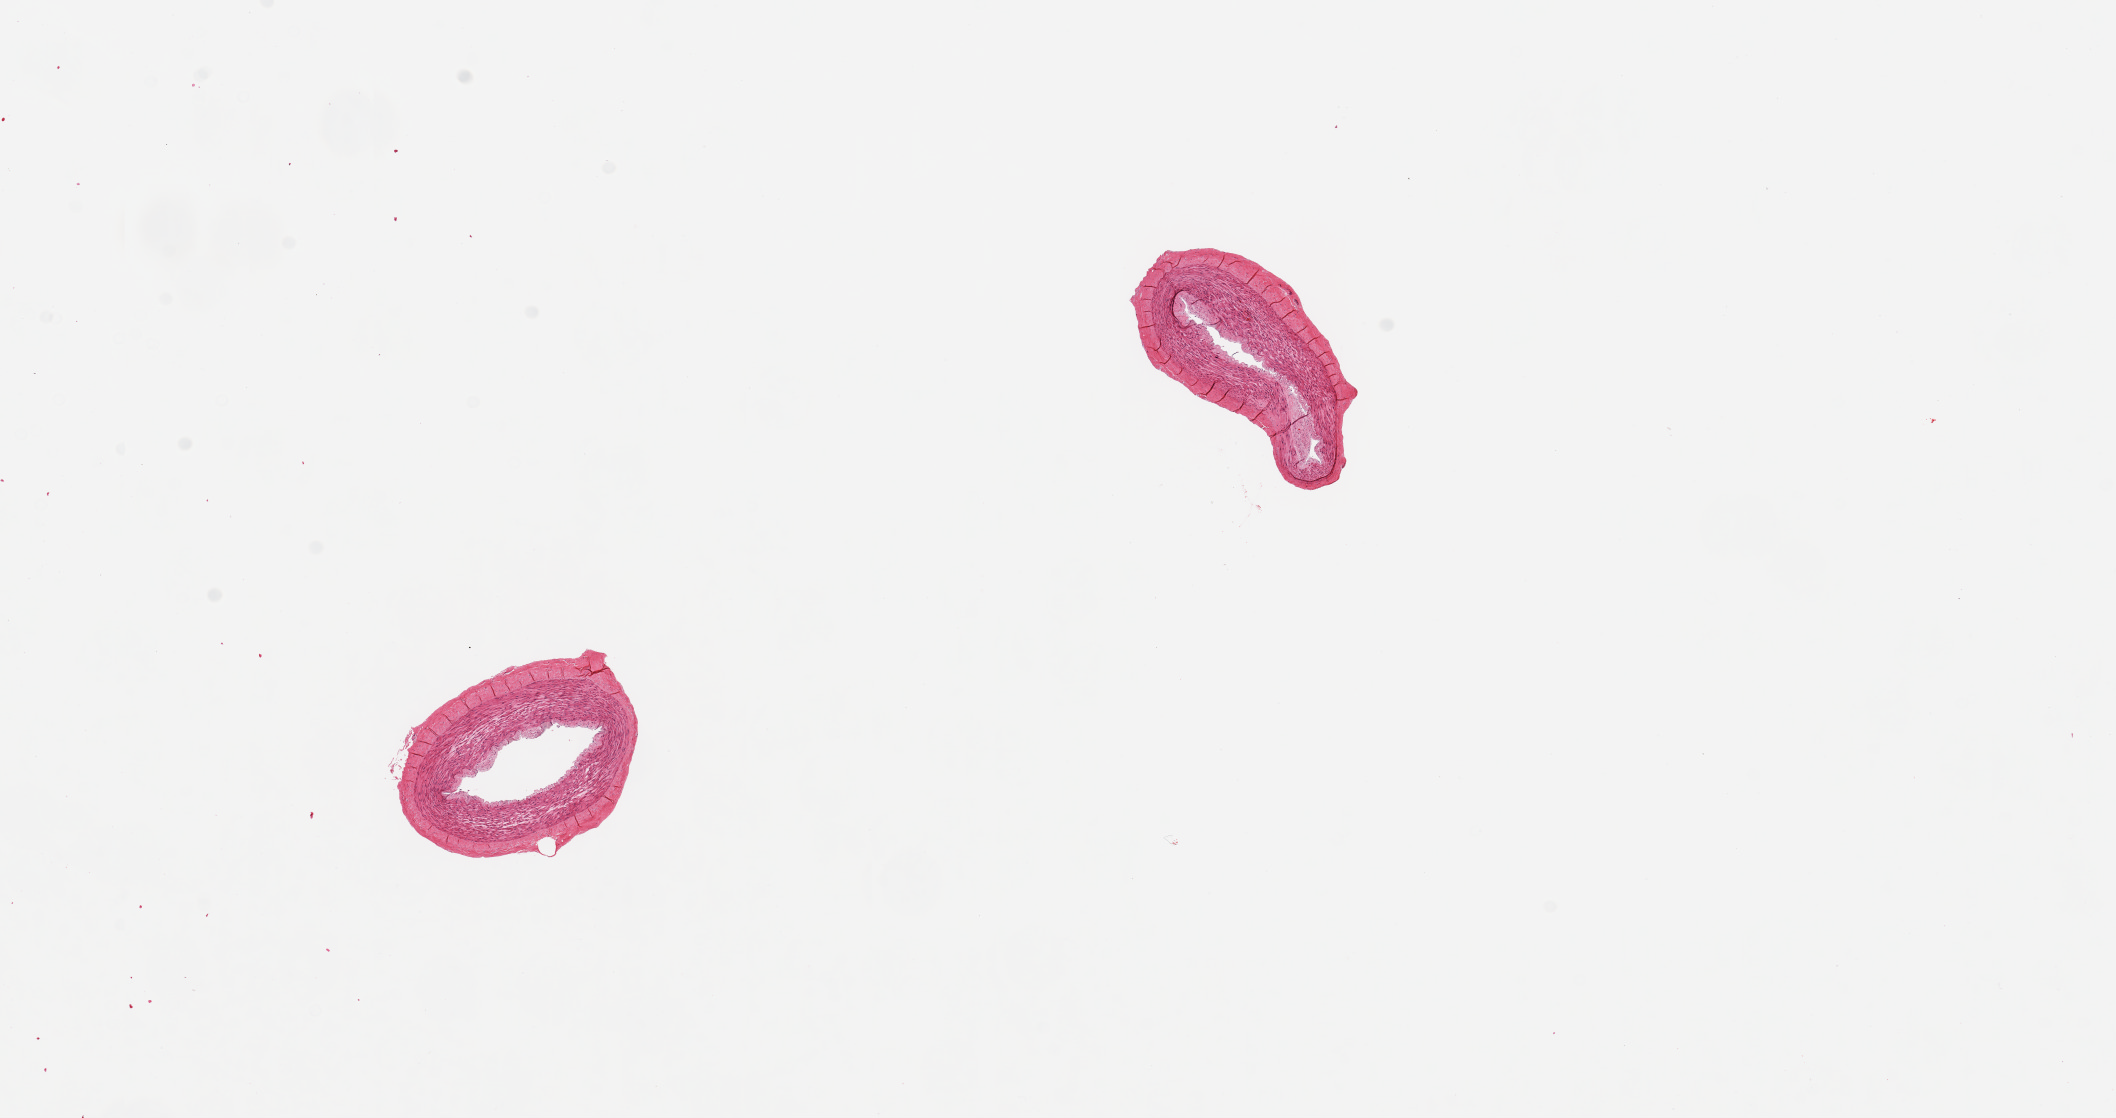
Digitized haematoxylin and eosin-stained section — low-resolution overview of the scanned area, about 16.7 x 8.8 mm; PAXgene-fixed, paraffin-embedded tissue; sampled site (target tissue): tibial artery; donor tissue sample. Donor sex: female.
Review note (as recorded): 2 pieces, 2x1 & 2x1mm; , clean specimens.